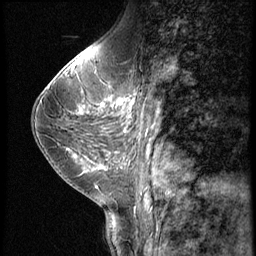
Breast MRI (dynamic contrast-enhanced), one sagittal slice. Slice 27 of 56 in the series (ordered by position). Dynamic contrast-enhanced series, image 2 of 3 at this slice position (ordered by acquisition). 1.5 T. TE 4.2 ms, TR 9 ms. 2.5 mm slice thickness. 256 × 256 image matrix, field of view 180 × 180 mm. Female patient, age 38 years. Case-level facts recorded for this patient, not image findings: setting: breast cancer imaged before/during neoadjuvant chemotherapy; receptor status: triple-negative.
Annotated regions visible in this slice (semi-automatic segmentation, software-assisted and operator-edited):
- analysis volume of interest (the breast-tissue region the enhancement analysis was run in; not a lesion): bounding box [x1, y1, x2, y2] px = [107, 95, 145, 149]
- tumour enhancement mask (voxels above the 140 % enhancement threshold inside the analysis volume of interest): [113, 98, 133, 106]